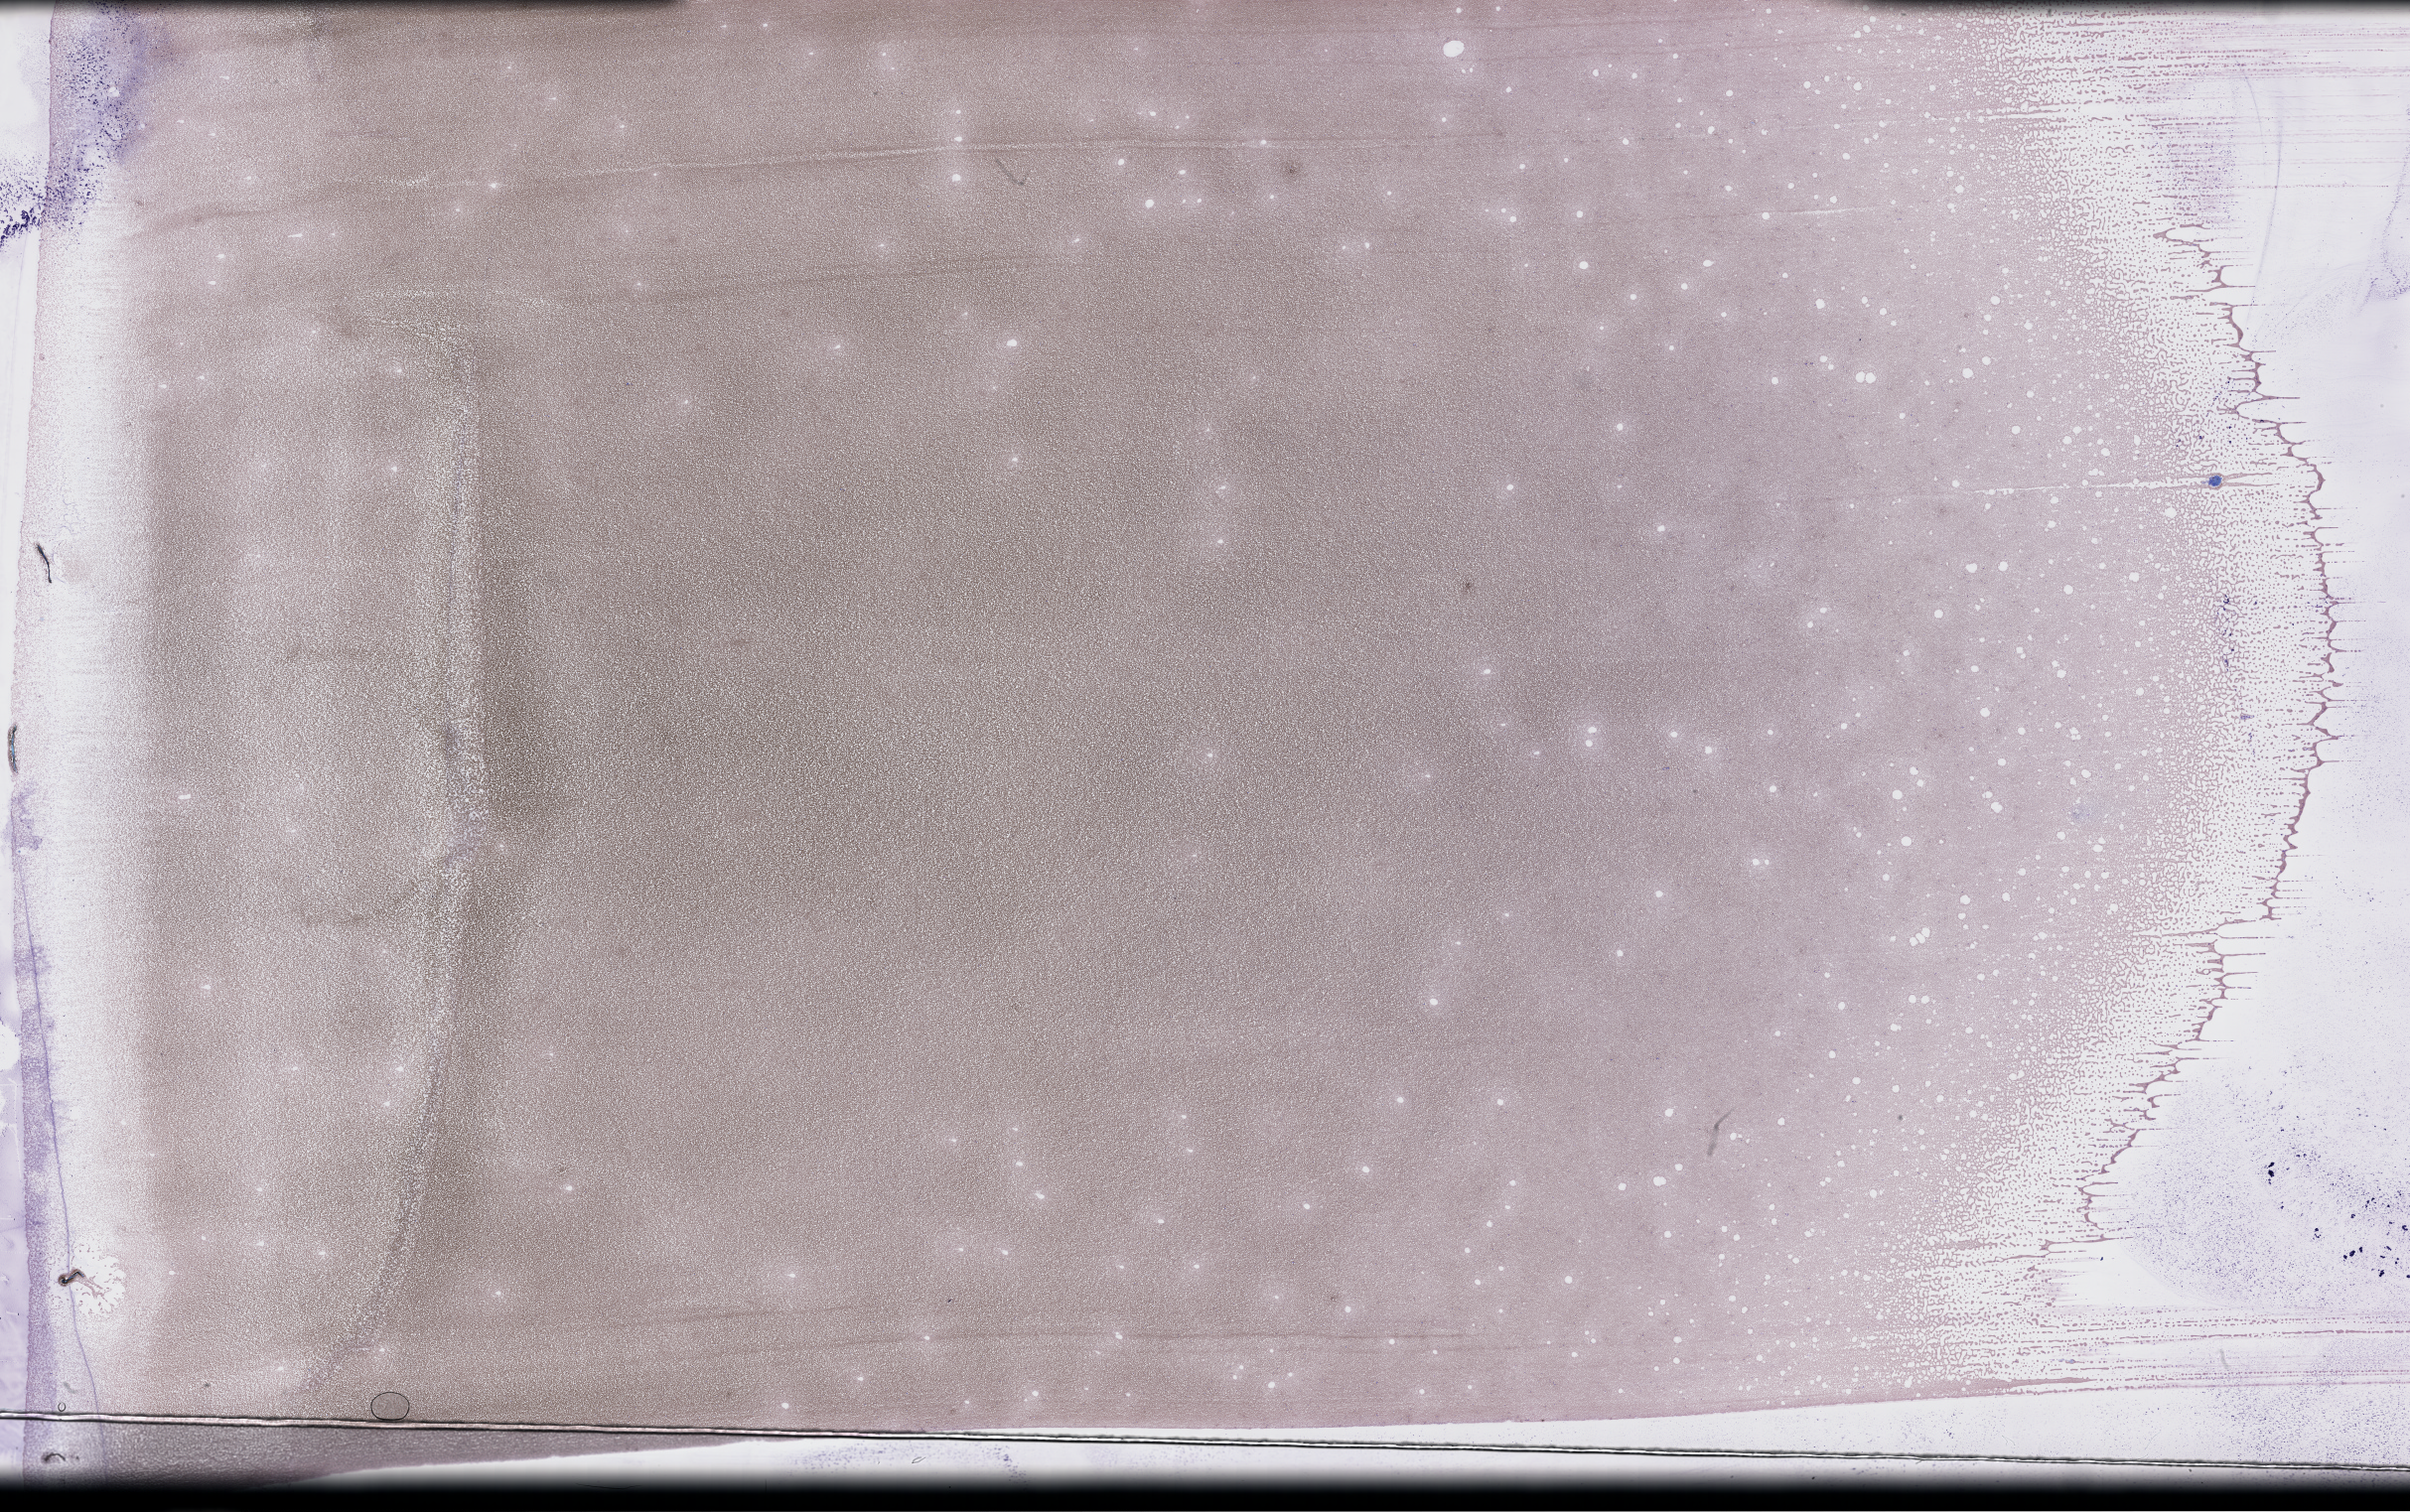
Wright-Giemsa-stained whole blood smear, whole-slide image, shown as a low-resolution overview of the whole scanned area (about 39.2 x 24.6 mm). EDTA-anticoagulated smear. Specimen time point: collected on treatment. Female patient.
- from a patient with: Plasma Cell Myeloma